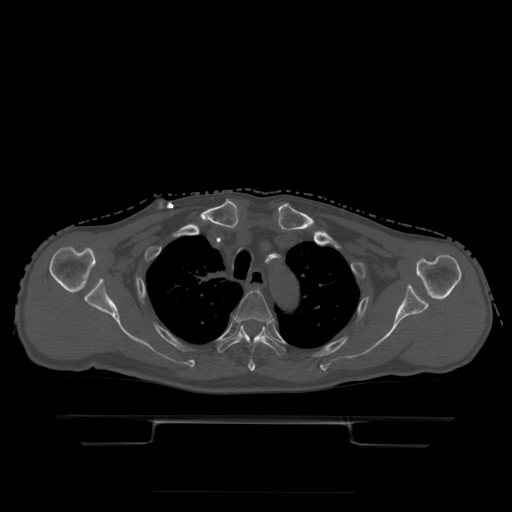
CT including the spine, one axial slice; slice 363 of 522 in the series (ordered by position); bone window (W 1800 / L 400 HU); 1.25 mm slice thickness; 512 × 512 image matrix. Patient age 68 years. From the clinical record (not read from this slice): primary cancer: urothelial.
Annotated regions visible in this slice (semi-automatically segmented with operator editing):
- T3 vertebra: bounding box [x1, y1, x2, y2] px = [236, 291, 273, 372]
- T4 vertebra: [217, 321, 286, 355]